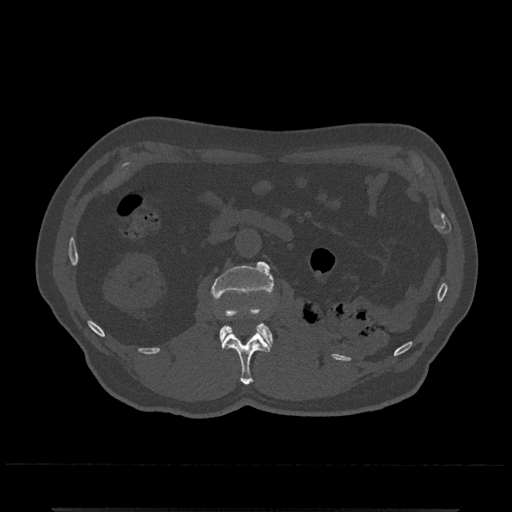
CT including the spine, one axial slice. Slice 328 of 797 in the series (ordered by position). Bone window (W 1800 / L 400 HU). 0.5 mm slice thickness. 512 × 512 image matrix, field of view 393 × 393 mm. Patient: male, 67 years. From the clinical record (not read from this slice): primary cancer: prostate.
Annotated regions visible in this slice (semi-automatic segmentation, software-assisted and operator-edited):
- L1 vertebra: box from (x=222, y=331) to (x=270, y=385) px
- L2 vertebra: (x=211, y=261)–(x=274, y=348)